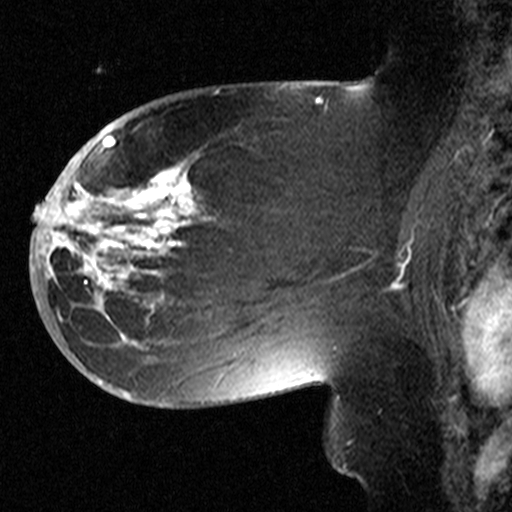
Breast MRI (dynamic contrast-enhanced), one sagittal slice; slice 22 of 44 in the series (ordered by position); dynamic contrast-enhanced study with each time point stored as its own series, time point 2 of 3 at this slice position (early post-contrast, ordered by acquisition time); 1.5 T; TE 4.5 ms, TR 11 ms; 3.27 mm slice thickness; 512 × 512 image matrix, field of view 200 × 200 mm. Female patient, age 53 years. From the clinical record (not read from this slice): setting: breast cancer imaged before/during neoadjuvant chemotherapy; receptor status: HR-positive, HER2-negative.
Annotated regions visible in this slice (semi-automatic segmentation, software-assisted and operator-edited):
- analysis volume of interest (the breast-tissue region the enhancement analysis was run in; not a lesion): box from (x=58, y=154) to (x=311, y=367) px
- tumour enhancement mask (voxels above the 90 % enhancement threshold inside the analysis volume of interest): (x=58, y=168)–(x=195, y=309)